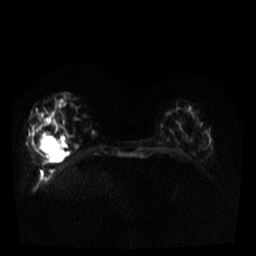
Breast MRI, one axial slice. Slice 11 of 34 in the series (ordered by position). Diffusion-weighted series; image 2 of 4 stored at this slice position (different b-values; order by instance number). 3 T. 256 × 256 image matrix. Female patient.
Outlined on this slice (expert manual segmentation):
- tumour on diffusion-weighted imaging: bounding box [x1, y1, x2, y2] px = [37, 134, 63, 155]